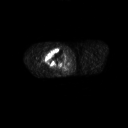
FDG PET of an extremity soft-tissue mass (from a PET/CT study), one axial slice. Slice 252 of 311 in the series (ordered by position). 128 × 128 image matrix, field of view 700 × 700 mm. Male patient, age 50 years. From the clinical record (not read from this slice): histological type: undifferentiated - pleiomorphic; grade: high; site of the primary tumour: right thigh.
Outlined on this slice (expert contour drawn on MRI and transferred to this co-registered scan by the dataset authors):
- gross tumour volume including surrounding oedema: bounding box [x1, y1, x2, y2] px = [42, 48, 65, 67]
- gross tumour volume (mass): [45, 49, 65, 66]